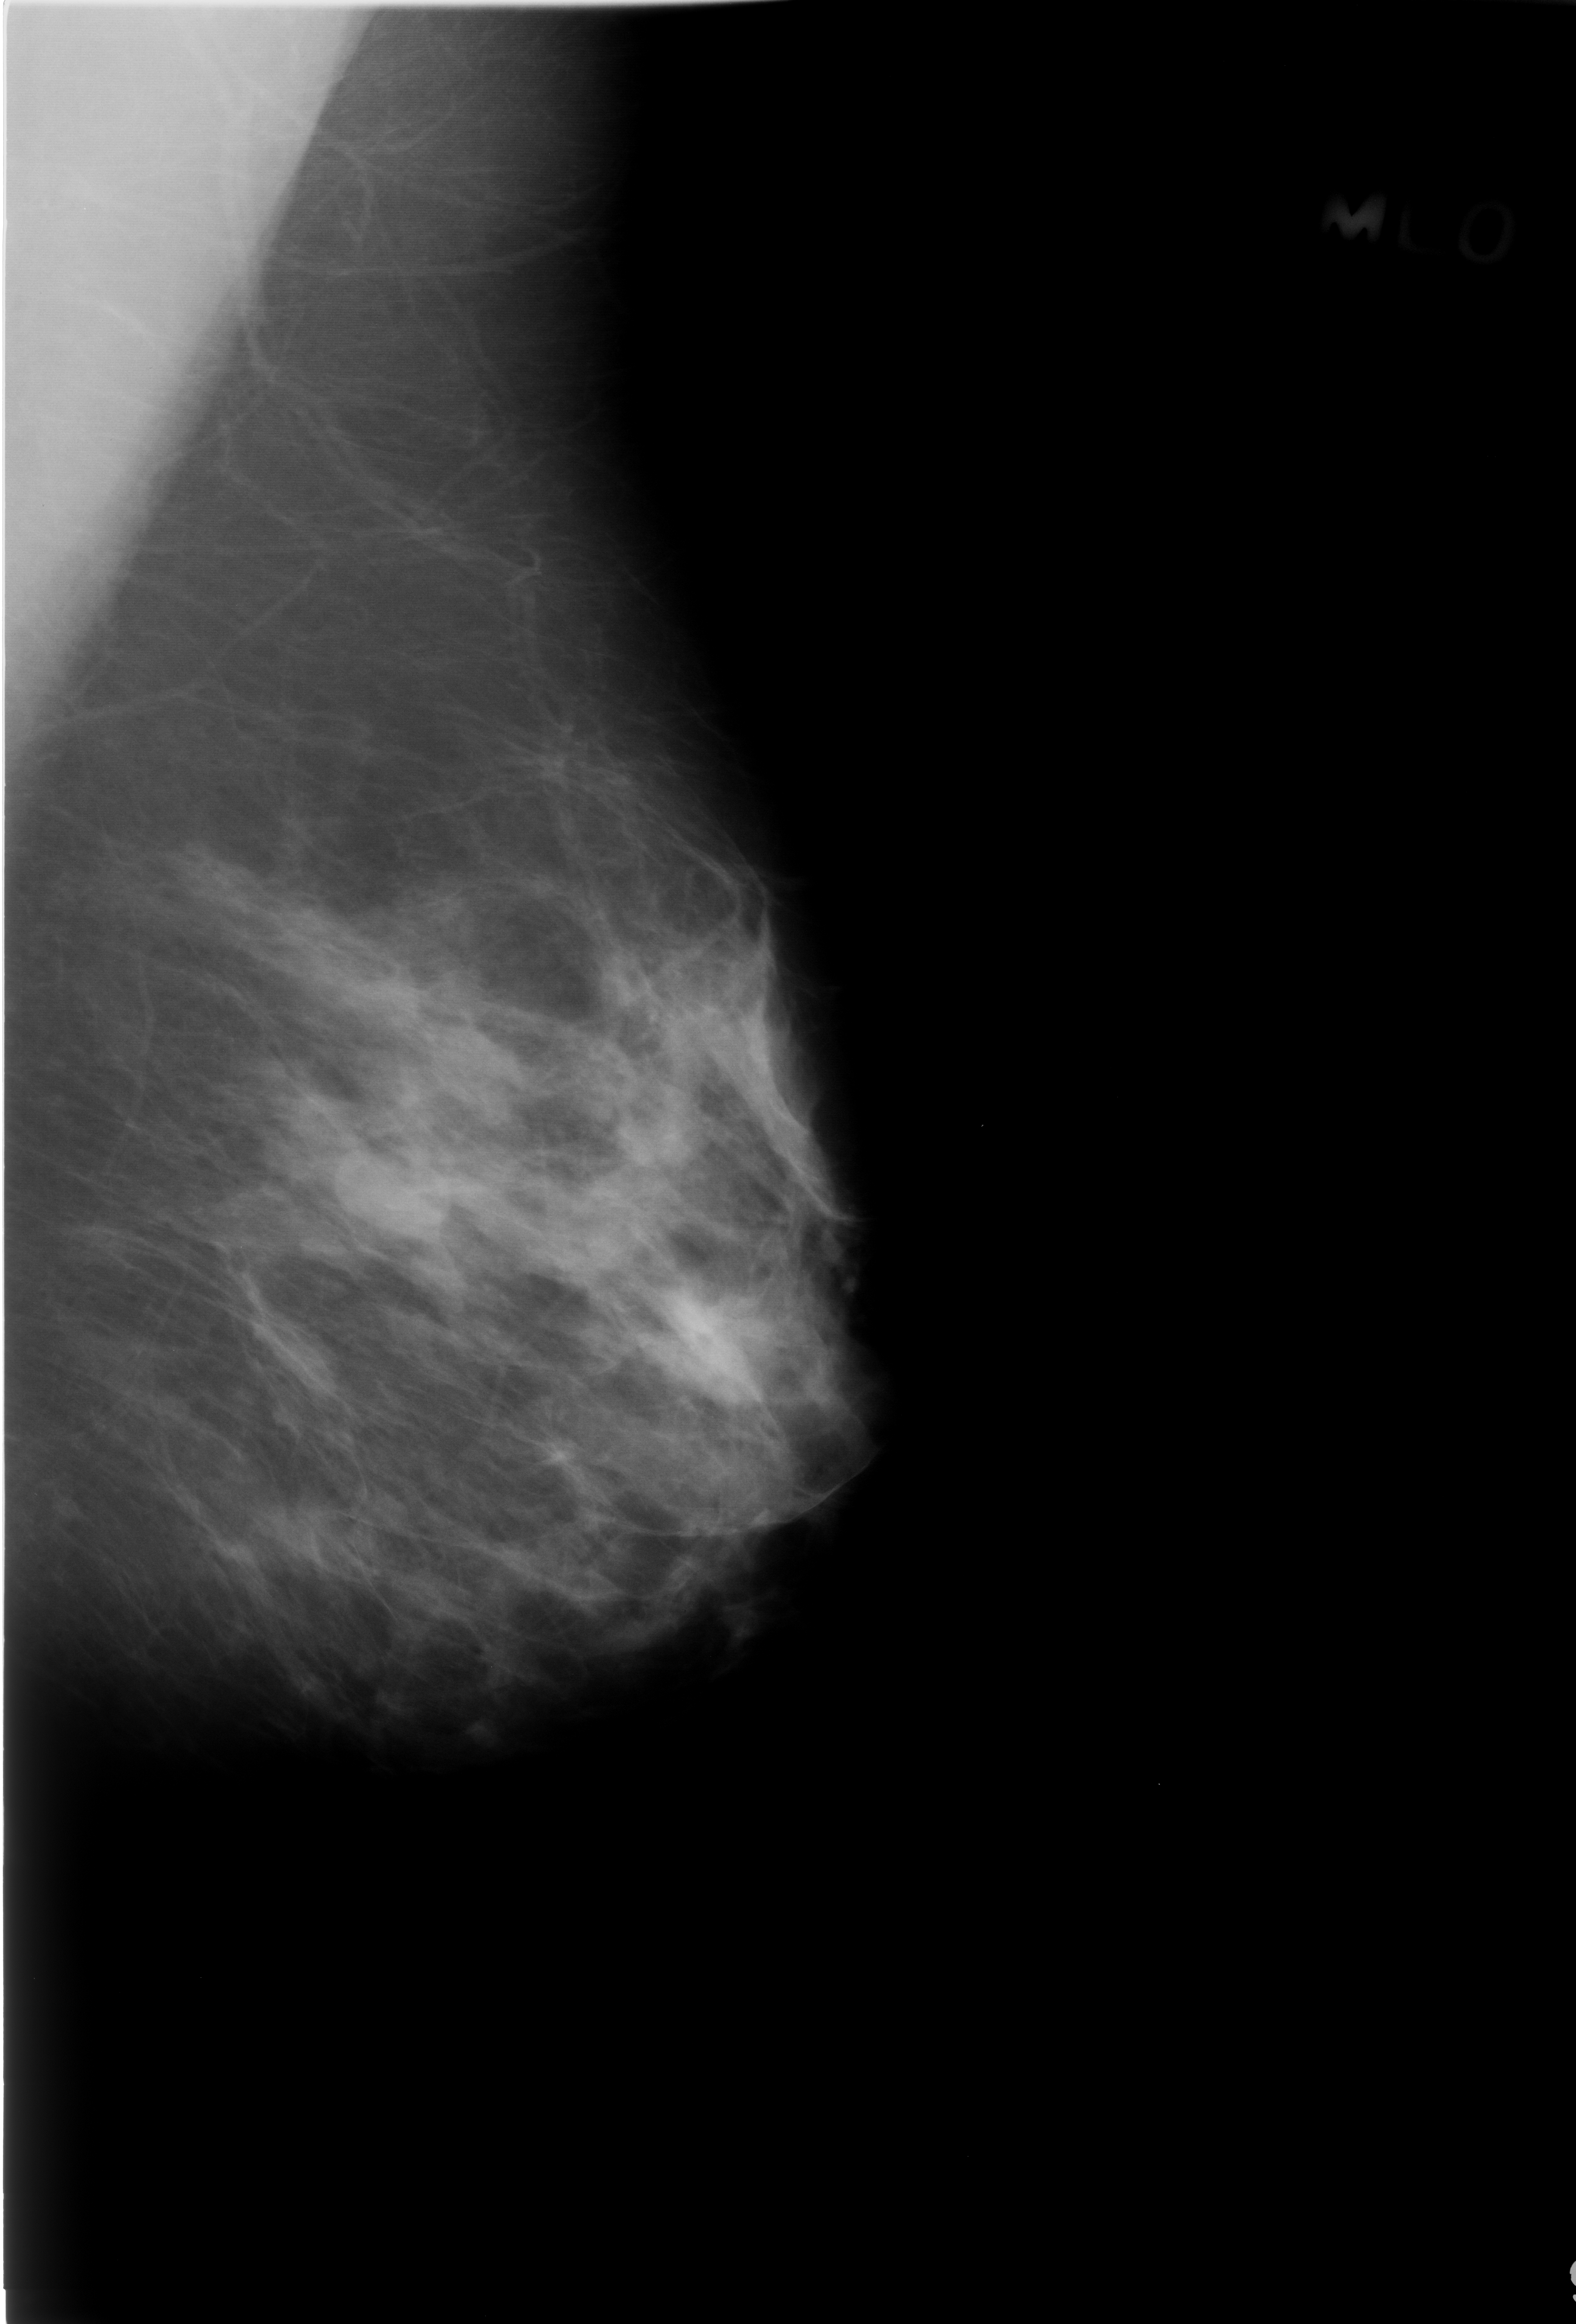
Scanned film-screen mammogram, left breast, mediolateral oblique (MLO) view.
Abnormality record for this image: mass, shape oval, margins circumscribed; BI-RADS assessment category 3; subtlety rating 4 on a 1 (subtle) to 5 (obvious) scale; pathology (as recorded): benign.